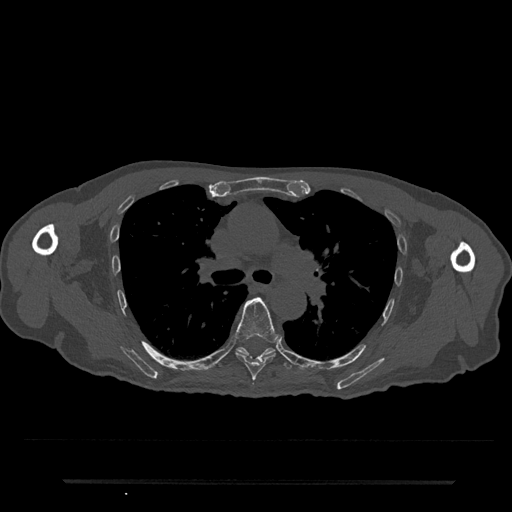
CT including the spine, one axial slice; position 517 of 797 along the scan axis; reconstruction kernel Br40s/3; 120 kVp; bone window (W 1800 / L 400 HU); 512 × 512 image matrix, field of view 427 × 427 mm. Patient: male, 74 years. Case-level facts recorded for this patient, not image findings: primary cancer: prostate.
Structures marked on this image (semi-automatic segmentation, software-assisted and operator-edited):
- T6 vertebra: bounding box [x1, y1, x2, y2] px = [234, 297, 279, 381]
- T7 vertebra: [218, 347, 292, 370]